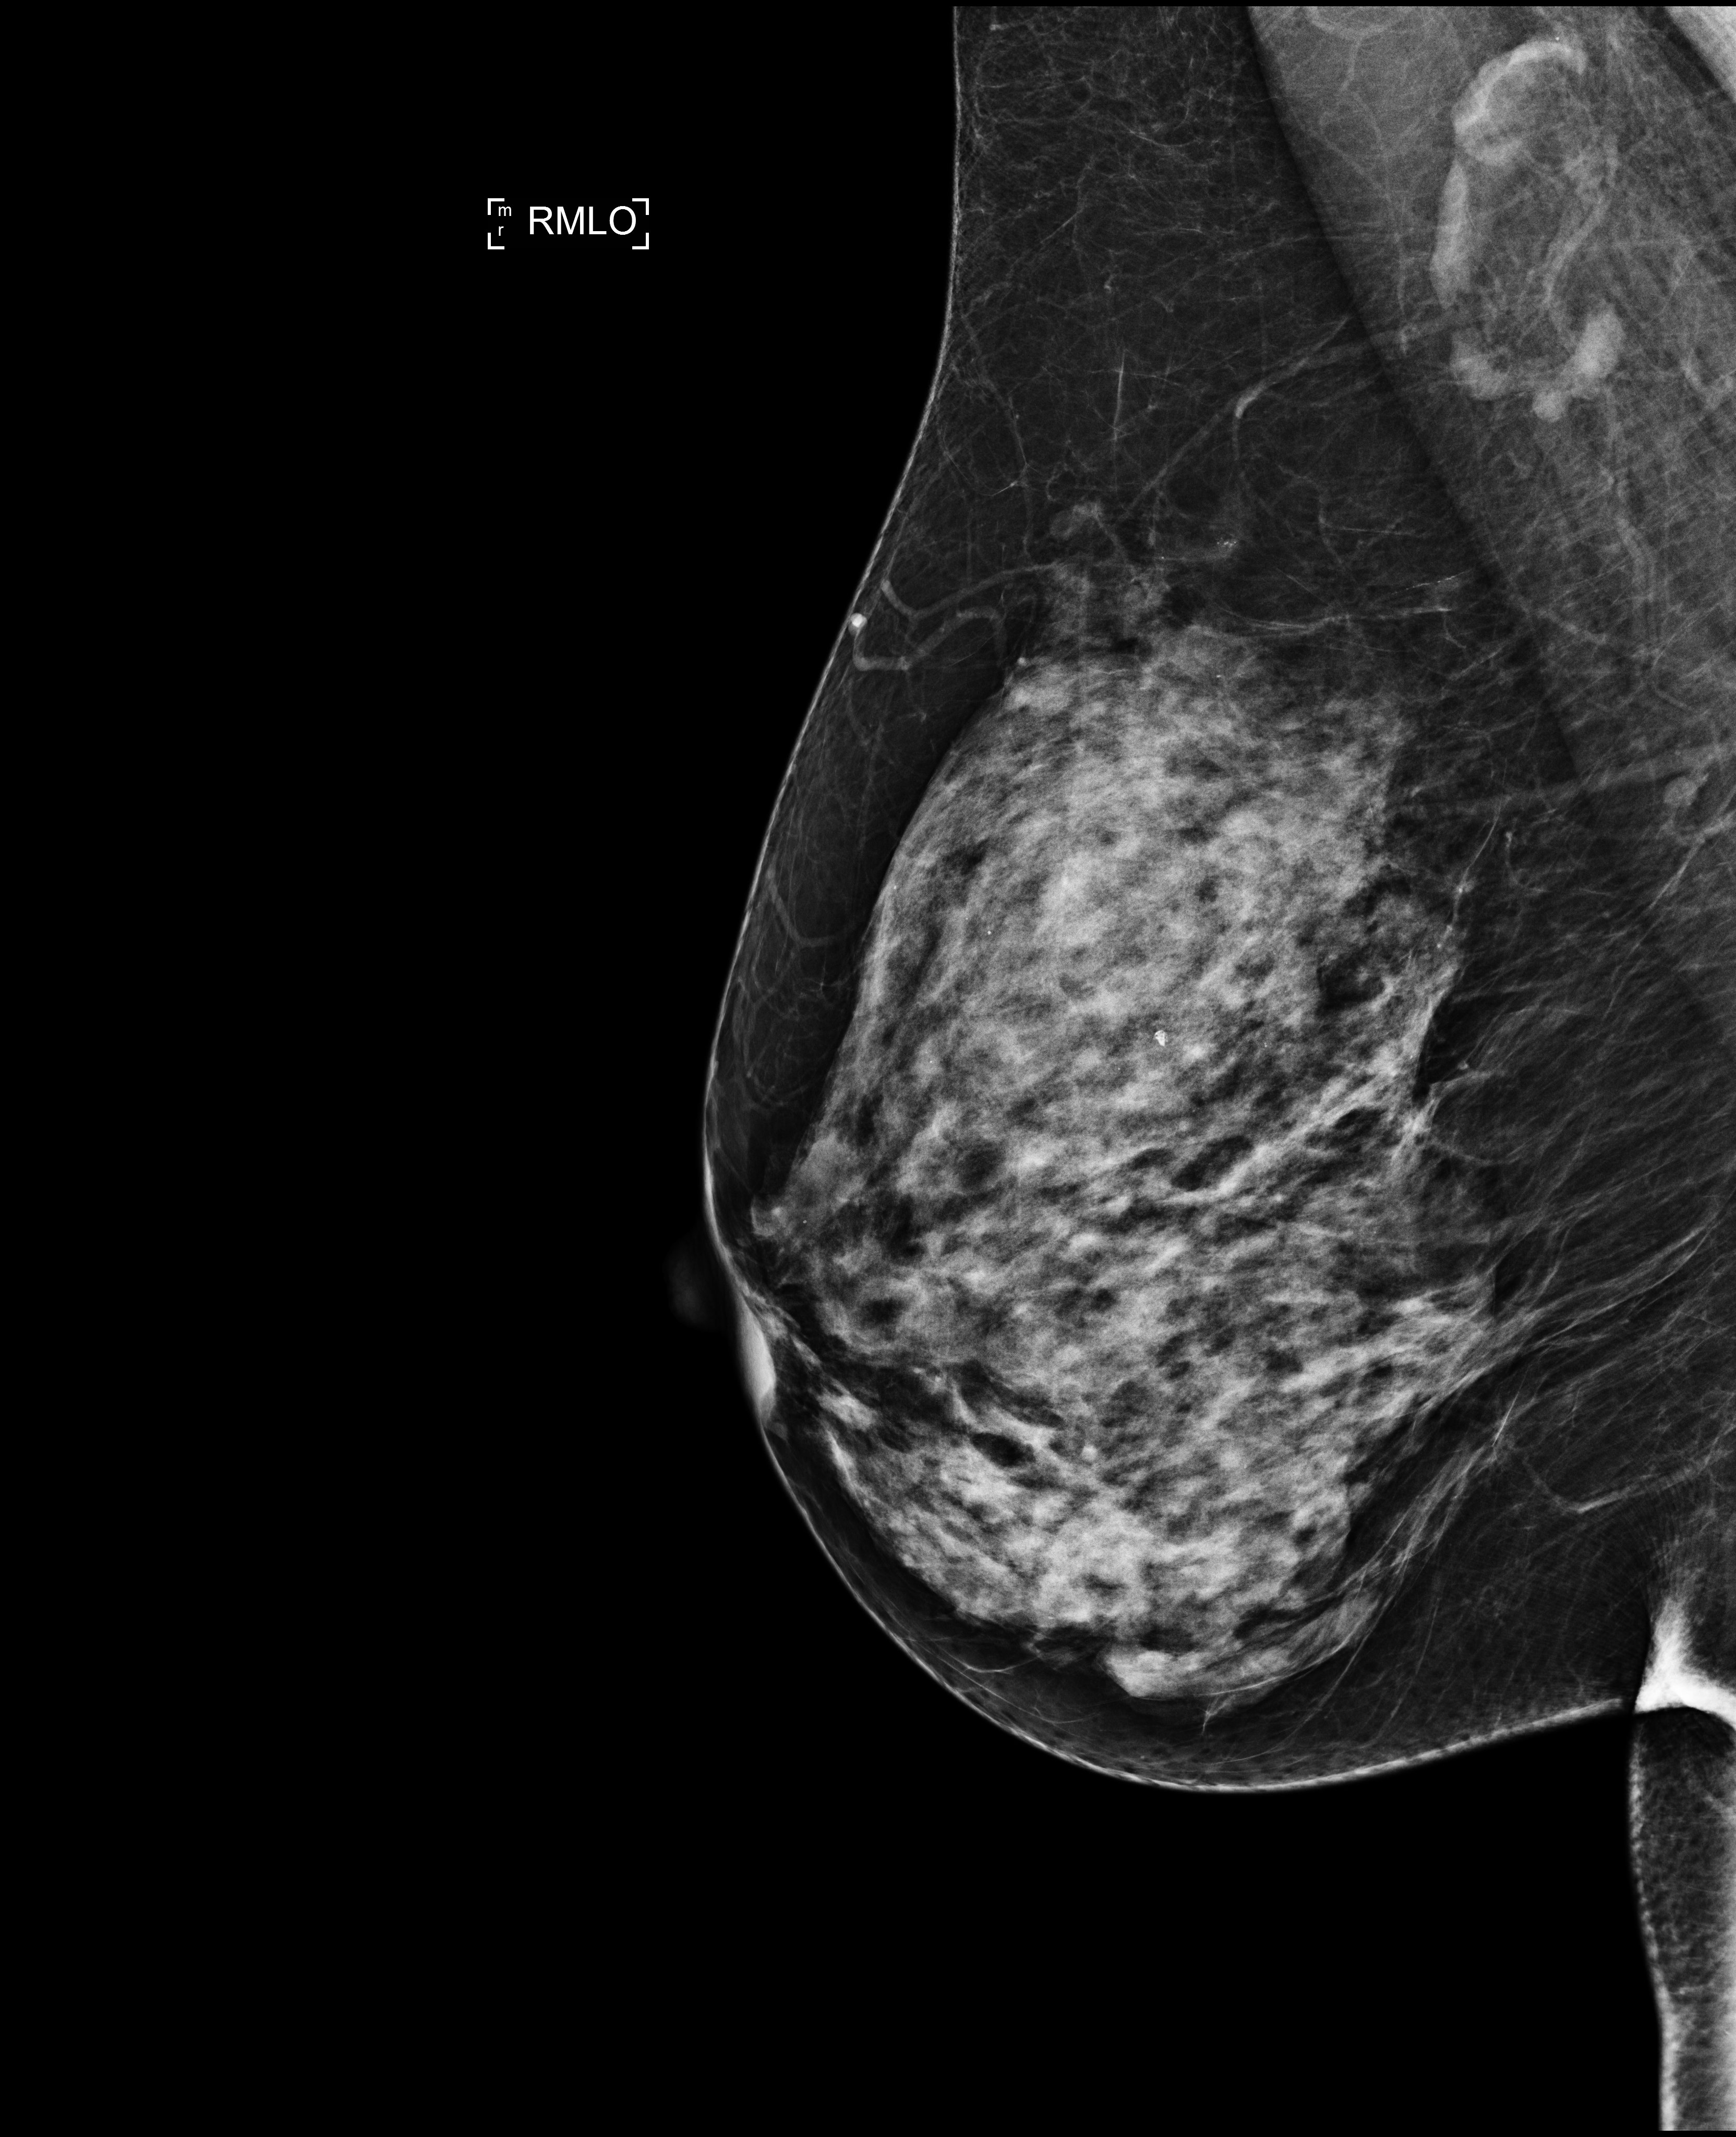
Annual screening mammography examination; compressed breast thickness 62 mm; system: Selenia Dimensions. Female patient, age 57 years.
Image type: full-field digital mammogram. Breast: right. Projection: MLO view.